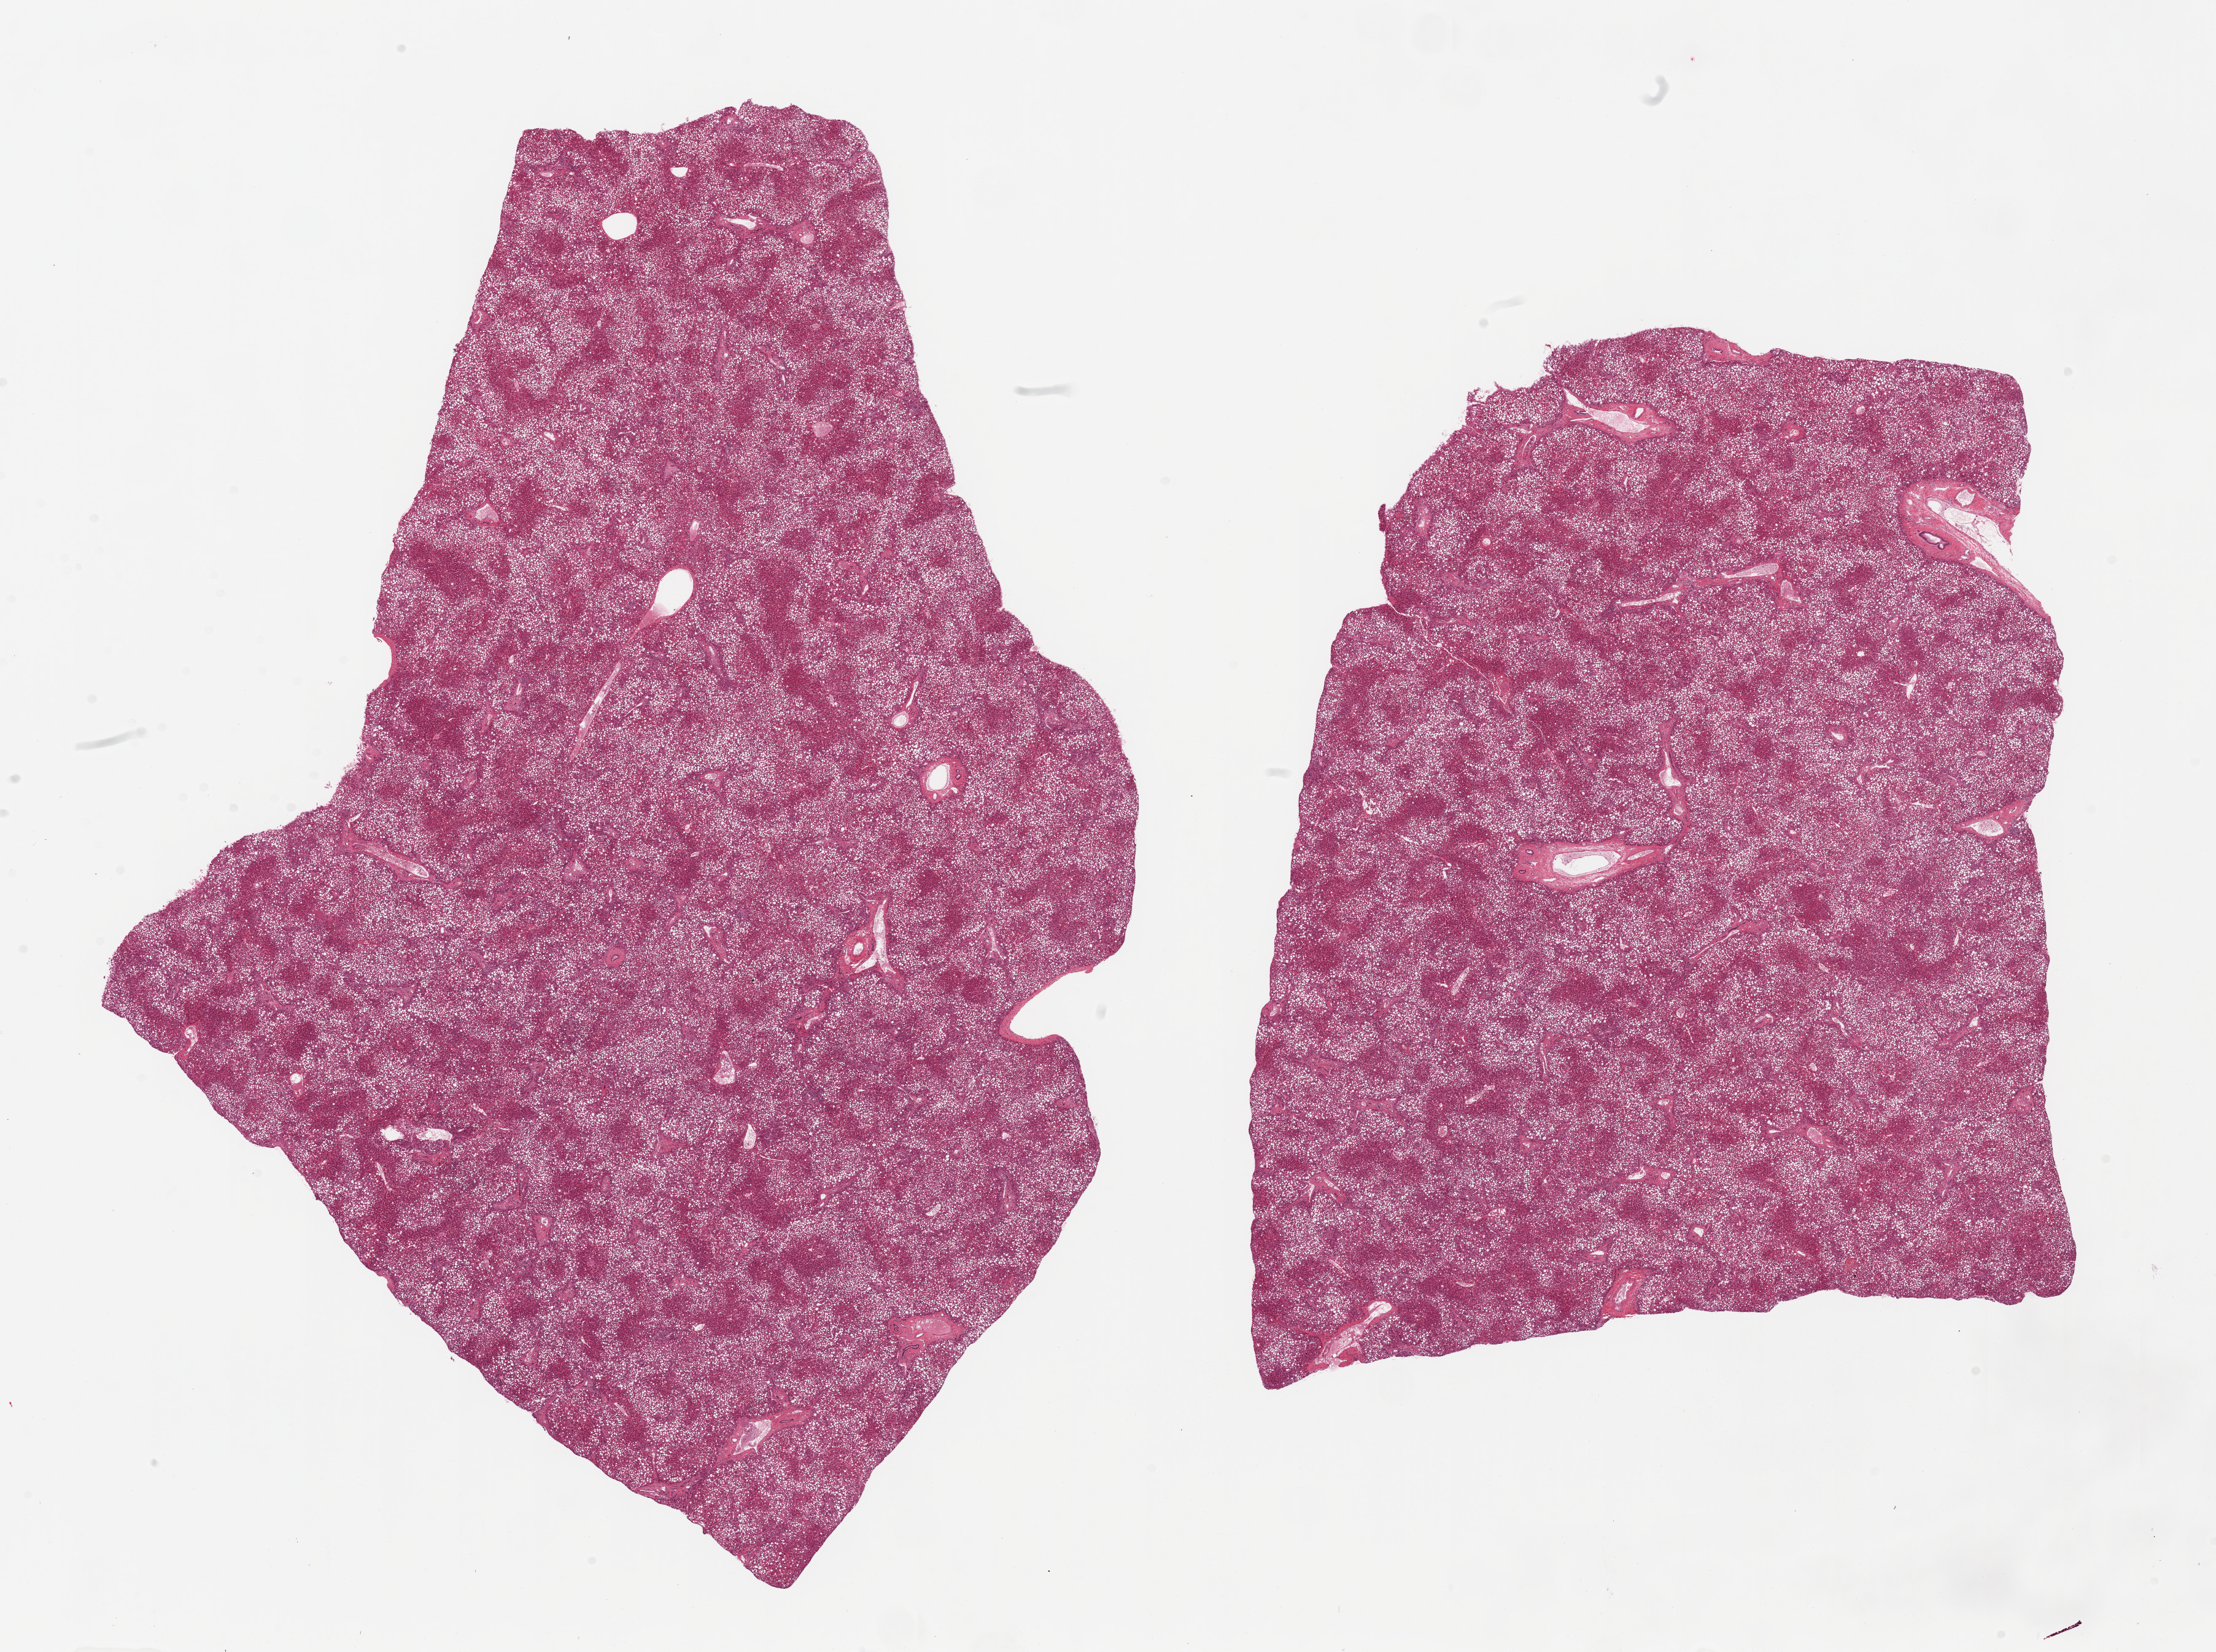
Digitized hematoxylin and eosin (H&E)-stained section, low-resolution overview of the scanned area, about 28.5 x 21.3 mm; PAXgene-fixed, paraffin-embedded tissue; target tissue: liver; donor tissue sample.
Reviewer comment on this tissue sample: 2 pieces; severe microvescicular and macrovesicular (predominant) steatosis, mild fibrosis.